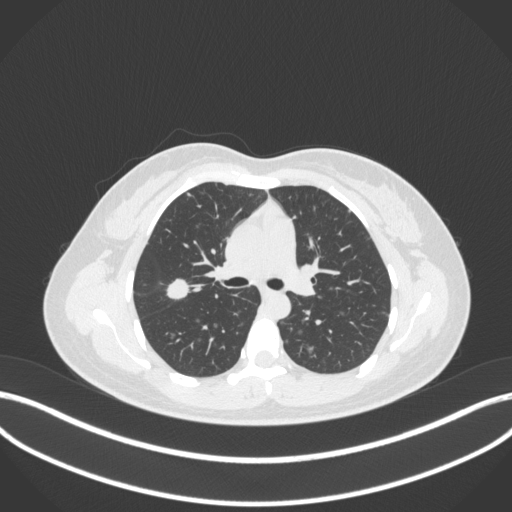
Chest CT, one axial slice. Position 210 of 214 along the scan axis. Reconstruction kernel B31f. 120 kVp. Lung window (W 1500 / L -600 HU). 1 mm slice thickness. 512 × 512 image matrix. Female patient, age 33 years. Case-level facts recorded for this patient, not image findings: clinical TNM (as recorded): T1c N0 M0; histopathological grade: G2-G3.
Structures marked on this image (rectangle marked by the reading radiologist):
- lung tumour (recorded histology: adenocarcinoma): bounding box <159,272,189,305> (left, top, right, bottom; pixels)